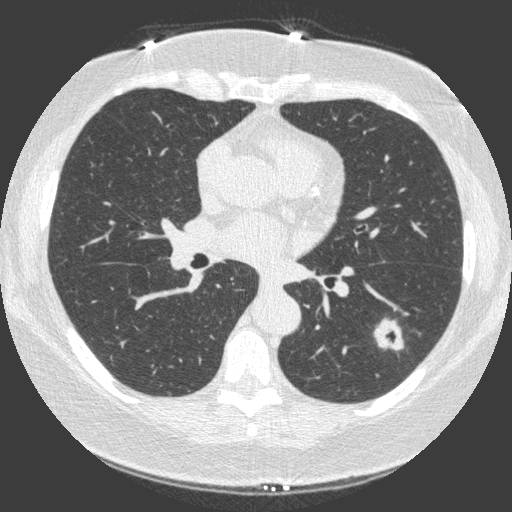
Low-dose screening chest CT, axial slice; third annual screen; lung window (W 1500 / L -600 HU); 120 kVp; slice 65 of 149 in the series. Female participant, aged 66 years at enrolment. Current smoker at enrolment.
Lesion marked by an expert reader, bounding box <363,302,420,355> (left, top, right, bottom; pixels). Reader record for this screening exam (exam-level; its link to the box is not recorded): non-calcified nodule or mass ≥4 mm, left lower lobe, 23 × 17 mm, spiculated (stellate) margins, soft tissue attenuation, pre-existing on the prior screen: yes; interval growth: yes. Official screen result: positive, other. Later outcome: lung cancer diagnosed 15 days after this screen — non-small cell carcinoma, left lower lobe, poorly differentiated (G3), stage IA (AJCC 6th edition), 20 mm at pathology.